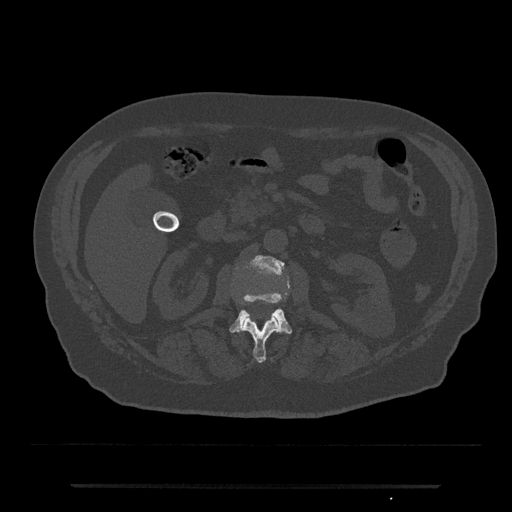
CT including the spine, one axial slice; position 503 of 797 along the scan axis; reconstruction kernel Br40s/3; bone window (W 1800 / L 400 HU); 0.5 mm slice thickness; 512 × 512 image matrix, field of view 434 × 434 mm. Male patient, age 80 years. Case-level facts recorded for this patient, not image findings: primary cancer: prostate.
Structures marked on this image (semi-automatically segmented with operator editing):
- L1 vertebra: bounding box [x1, y1, x2, y2] px = [243, 317, 280, 363]
- L2 vertebra: [229, 256, 292, 334]